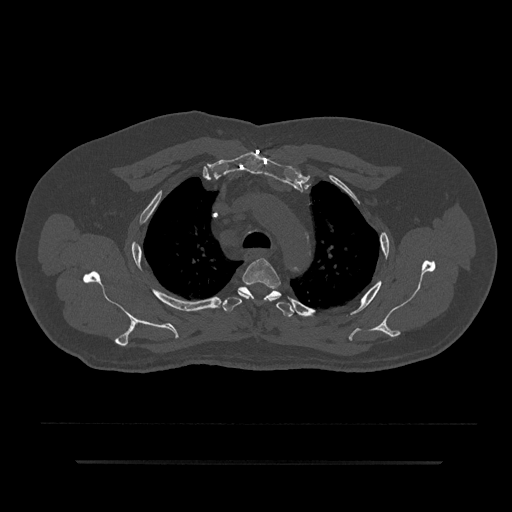
CT including the spine, one axial slice; position 641 of 797 along the scan axis; bone window (W 1800 / L 400 HU); 512 × 512 image matrix. Patient: male, 59 years. Case-level facts recorded for this patient, not image findings: primary cancer: bile ducts; vertebrae with lytic lesions (as recorded): T10.
Structures marked on this image (semi-automatically segmented with operator editing):
- T3 vertebra: bounding box [x1, y1, x2, y2] px = [238, 258, 281, 298]
- T4 vertebra: [222, 286, 294, 317]